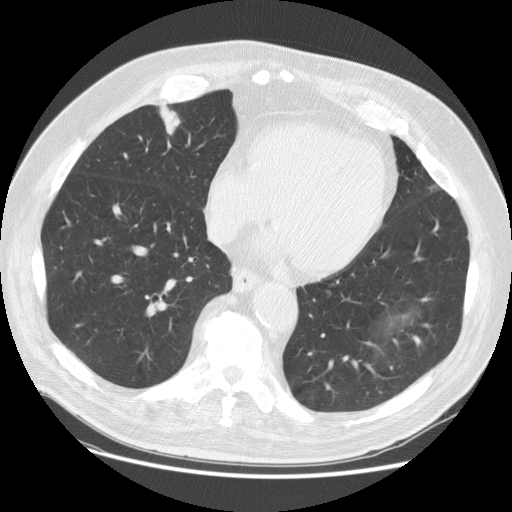
Low-dose screening chest CT, one axial slice. Slice 41 of 129 in the series (ordered by position). Reconstruction kernel STANDARD. 140 kVp. Lung window (W 1500 / L -600 HU). 2.5 mm slice thickness. 512 × 512 image matrix.
Outlined on this slice (expert manual segmentation):
- lesion 1 (tumor, upper lobe of right lung): bounding box [x1, y1, x2, y2] px = [159, 105, 181, 135]